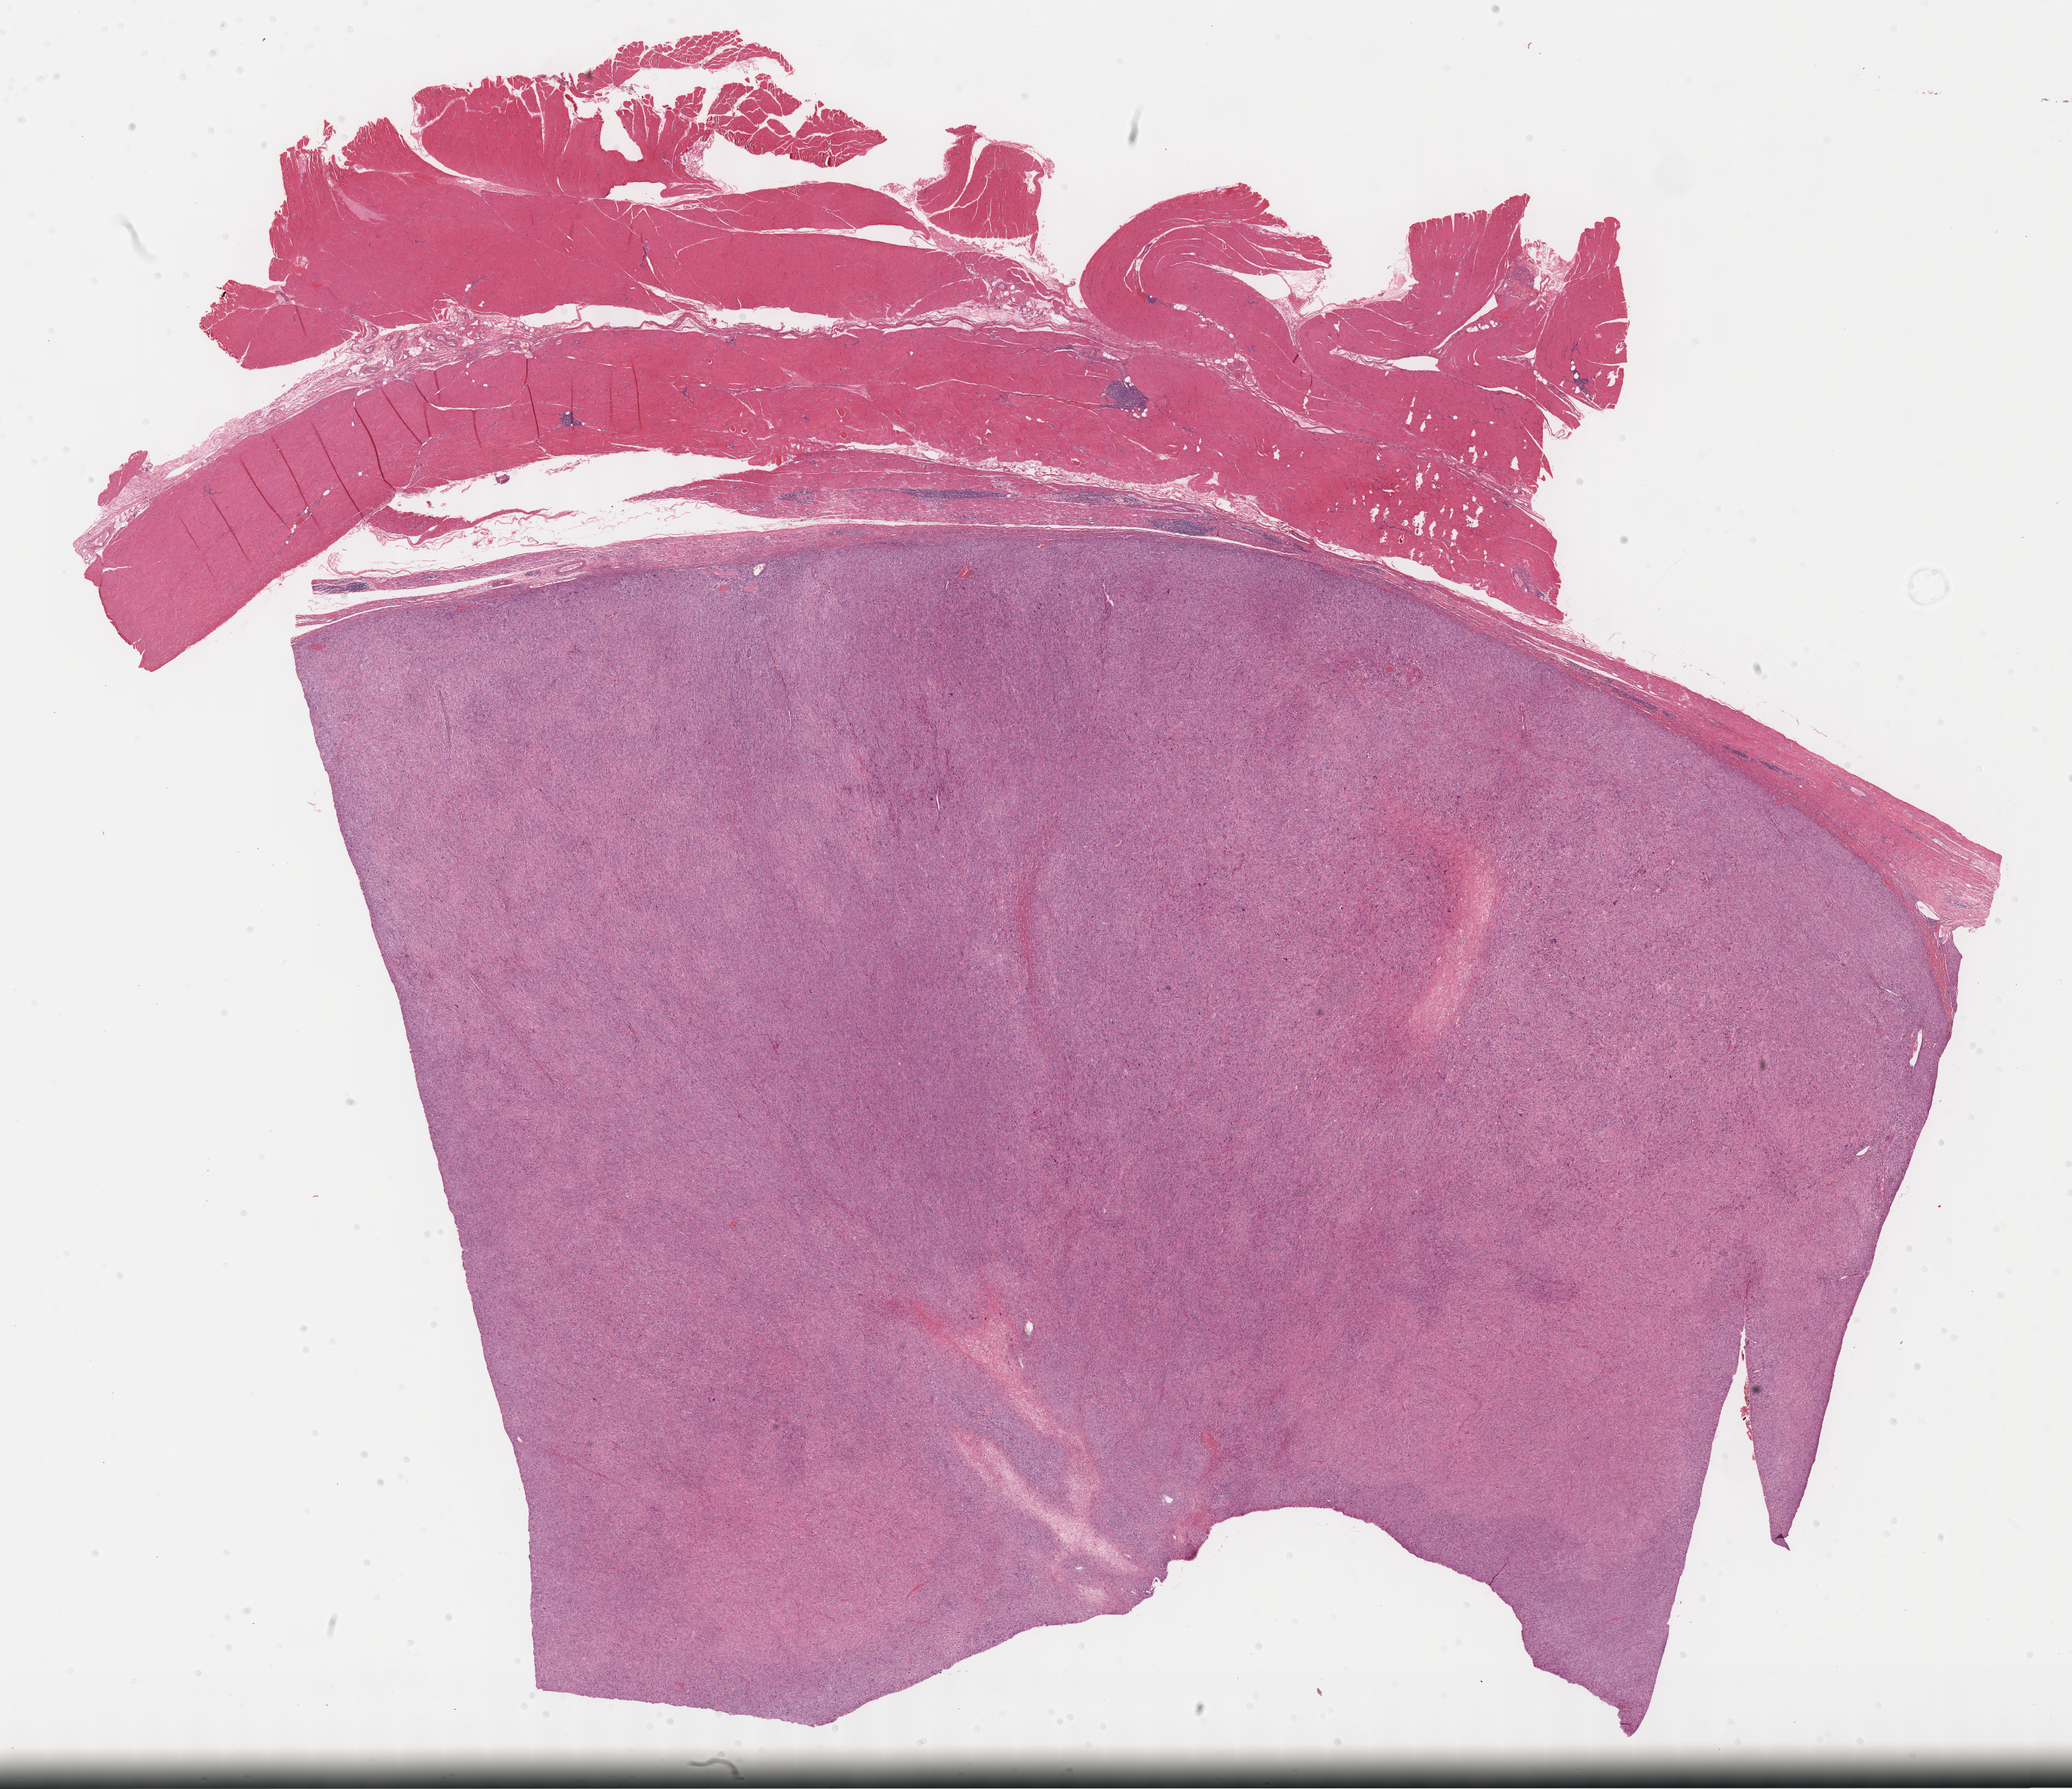
Whole-slide histology image, Hematoxylin and eosin (H&E) stained, low-resolution overview of the scanned area, about 23.7 x 20.4 mm, formalin-fixed paraffin-embedded (FFPE) diagnostic section, primary tumour sample from the connective, subcutaneous and other soft tissues. Patient: female, age at initial diagnosis 62 years.
Diagnosis: Malignant fibrous histiocytoma (connective, subcutaneous and other soft tissues of lower limb and hip).